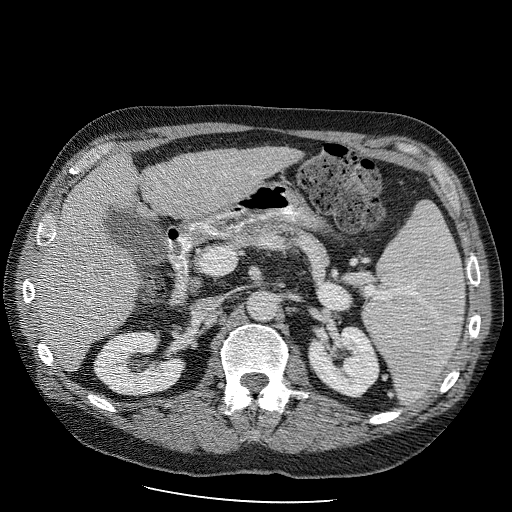
Contrast-enhanced abdominal CT (liver protocol), one axial slice. Position 45 of 98 along the scan axis. Soft-tissue window (W 400 / L 40 HU). 512 × 512 image matrix. Case-level facts recorded for this patient, not image findings: diagnosis: hepatocellular carcinoma (patient treated with transarterial chemoembolisation; whether this scan precedes or follows treatment is not stated here); TNM stage (as recorded): Stage-II; Child-Pugh class: B; tumour differentiation: moderately differentiated.
Outlined on this slice (semi-automatic segmentation, software-assisted and operator-edited):
- liver parenchyma outside the tumour (the mass and vessels are separate outlines, so this box may not span the whole liver): bounding box <32,146,301,370> (left, top, right, bottom; pixels)
- liver vessels: <45,233,90,305>